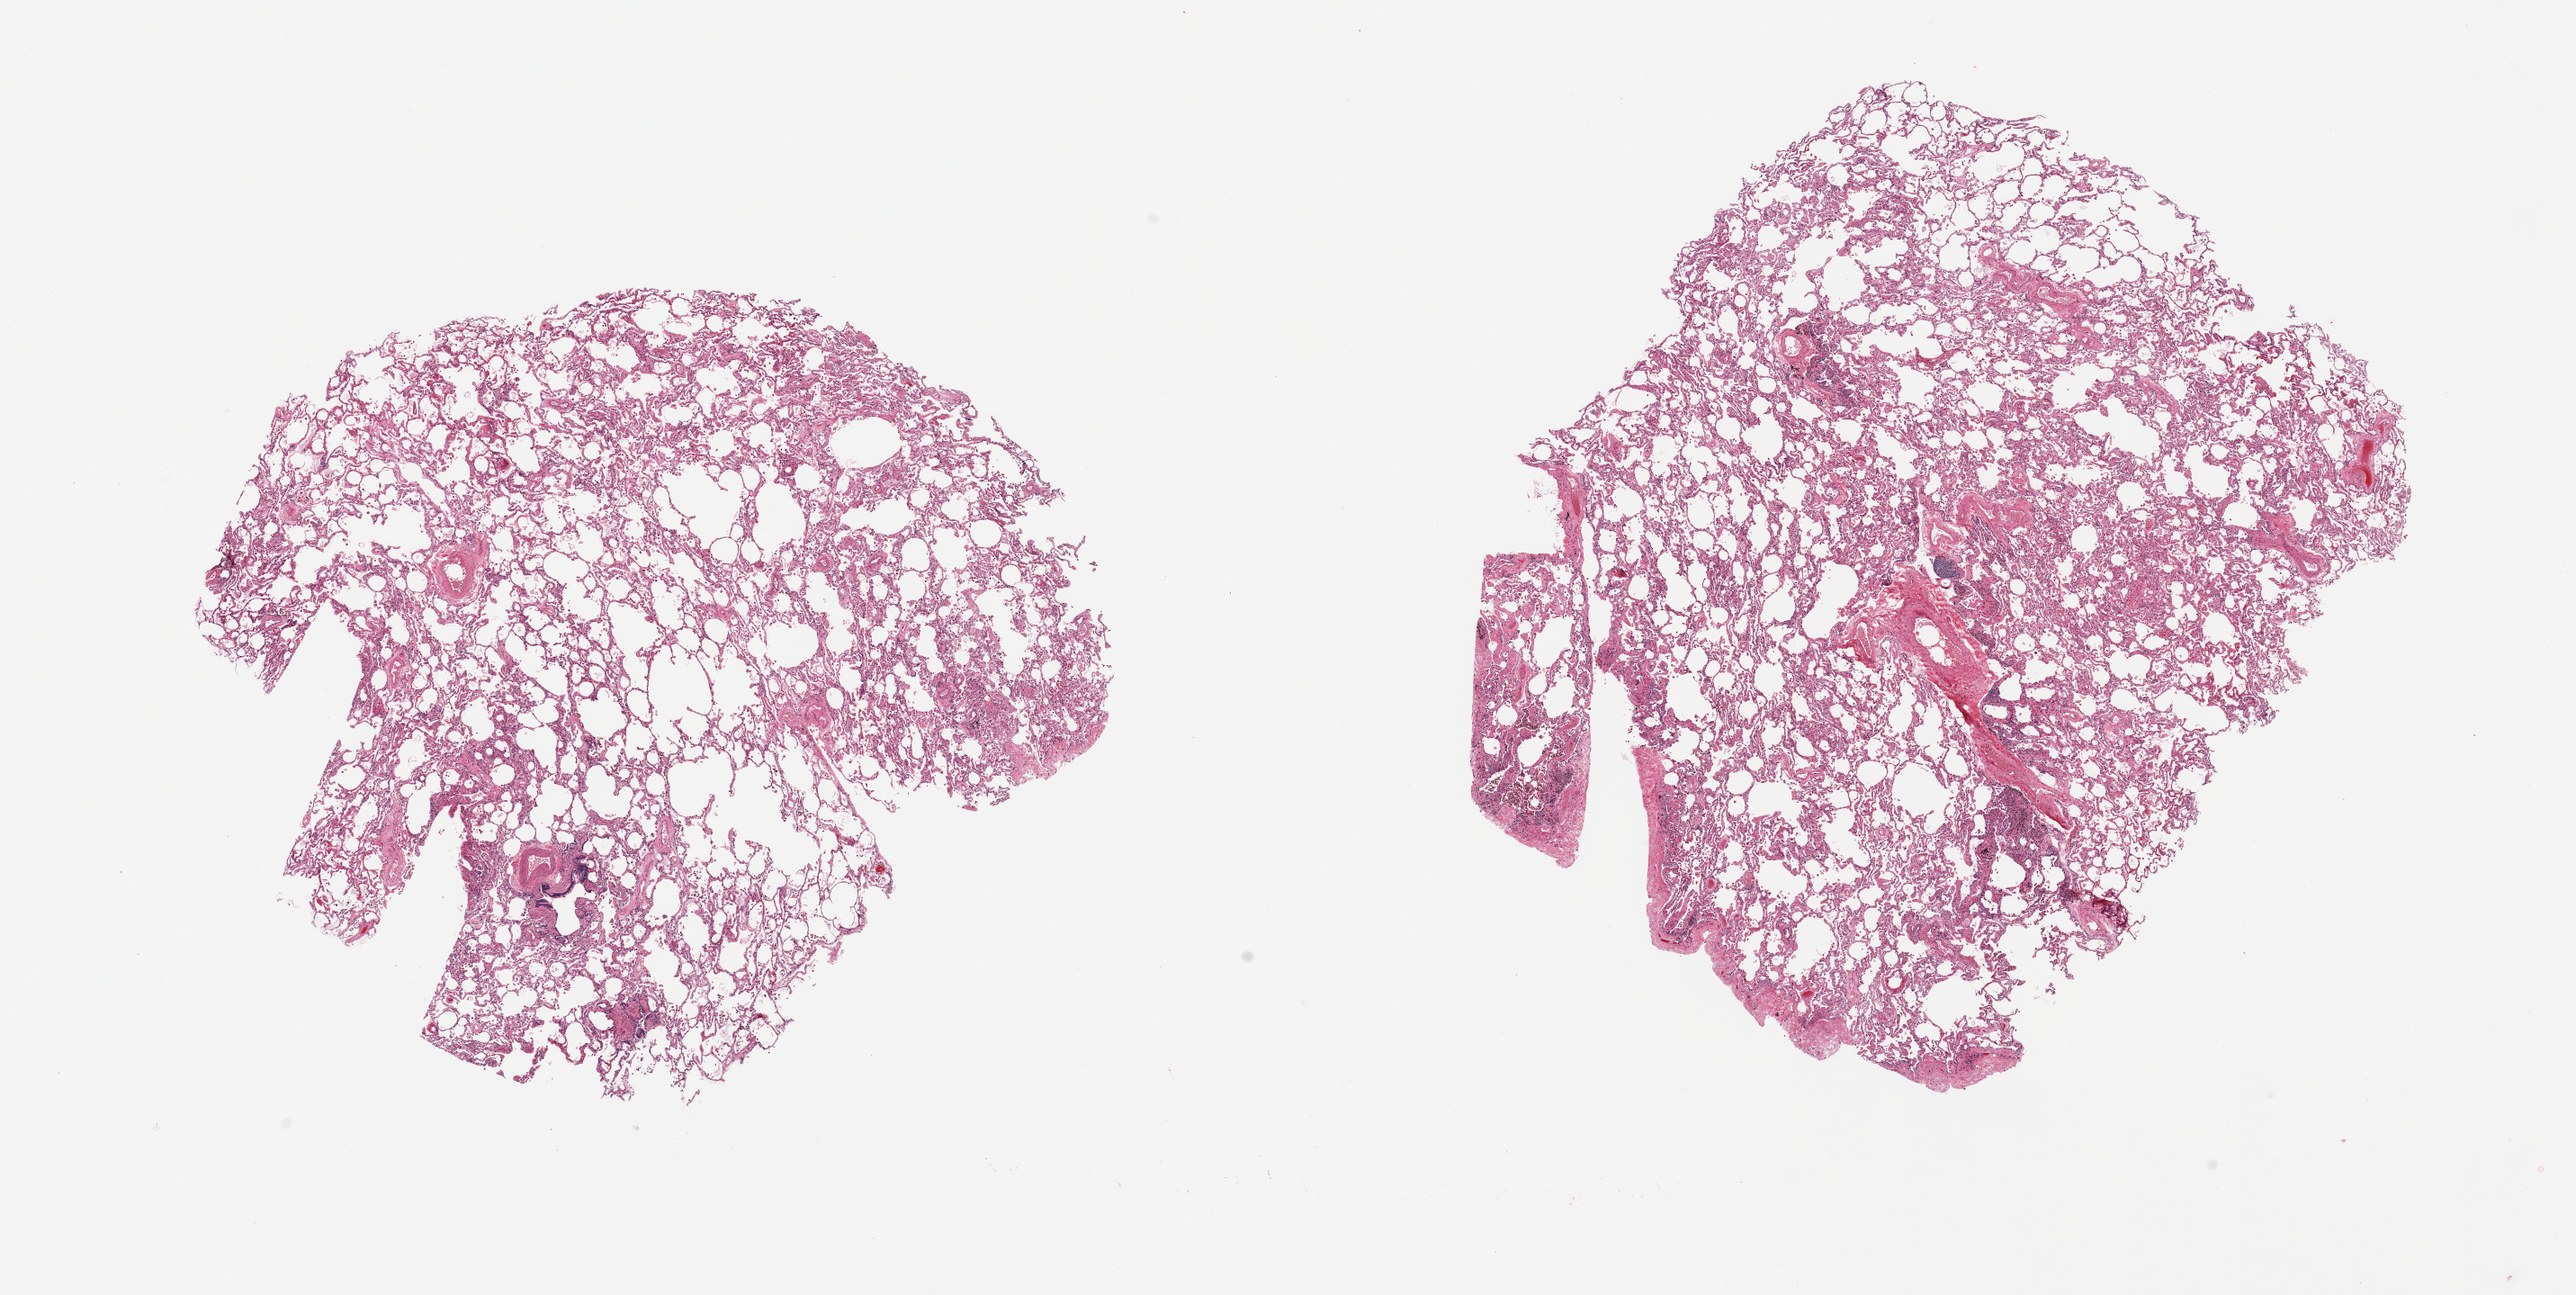
Whole-slide image, haematoxylin and eosin stain, low-resolution overview of the scanned area, about 22.6 x 11.4 mm. PAXgene-fixed, paraffin-embedded tissue. Sampled site (target tissue): lung. Tissue donor sample. Male donor.
Pathologist's review note for this sample: 2 pieces, mild congestion.